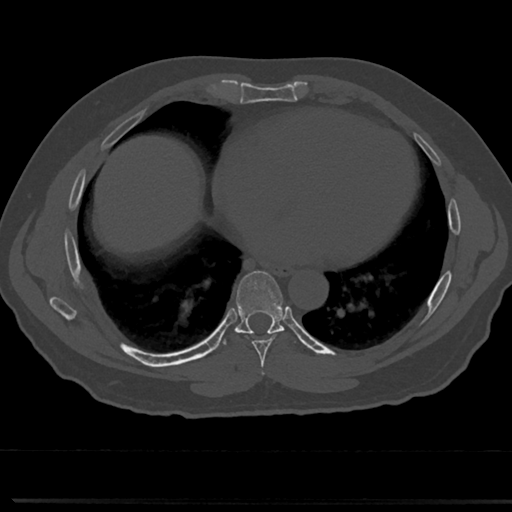
CT including the spine, one axial slice; slice 376 of 817 in the series (ordered by position); 120 kVp; bone window (W 1800 / L 400 HU); 0.5 mm slice thickness; 512 × 512 image matrix, field of view 355 × 355 mm. Patient: male, 61 years. Case-level facts recorded for this patient, not image findings: primary cancer: prostate.
Outlined on this slice (semi-automatic segmentation, software-assisted and operator-edited):
- T6 vertebra: bounding box <261,370,265,374> (left, top, right, bottom; pixels)
- T7 vertebra: <233,272,290,355>
- T8 vertebra: <239,326,280,332>